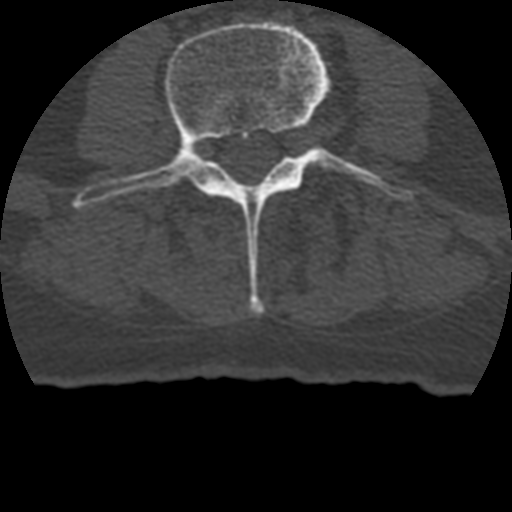
CT including the spine, one axial slice; bone window (W 1800 / L 400 HU); 512 × 512 image matrix, field of view 160 × 160 mm. Patient age 69 years. From the clinical record (not read from this slice): primary cancer: prostate.
Structures marked on this image (semi-automatic segmentation, software-assisted and operator-edited):
- L3 vertebra: bounding box [x1, y1, x2, y2] px = [77, 21, 410, 314]